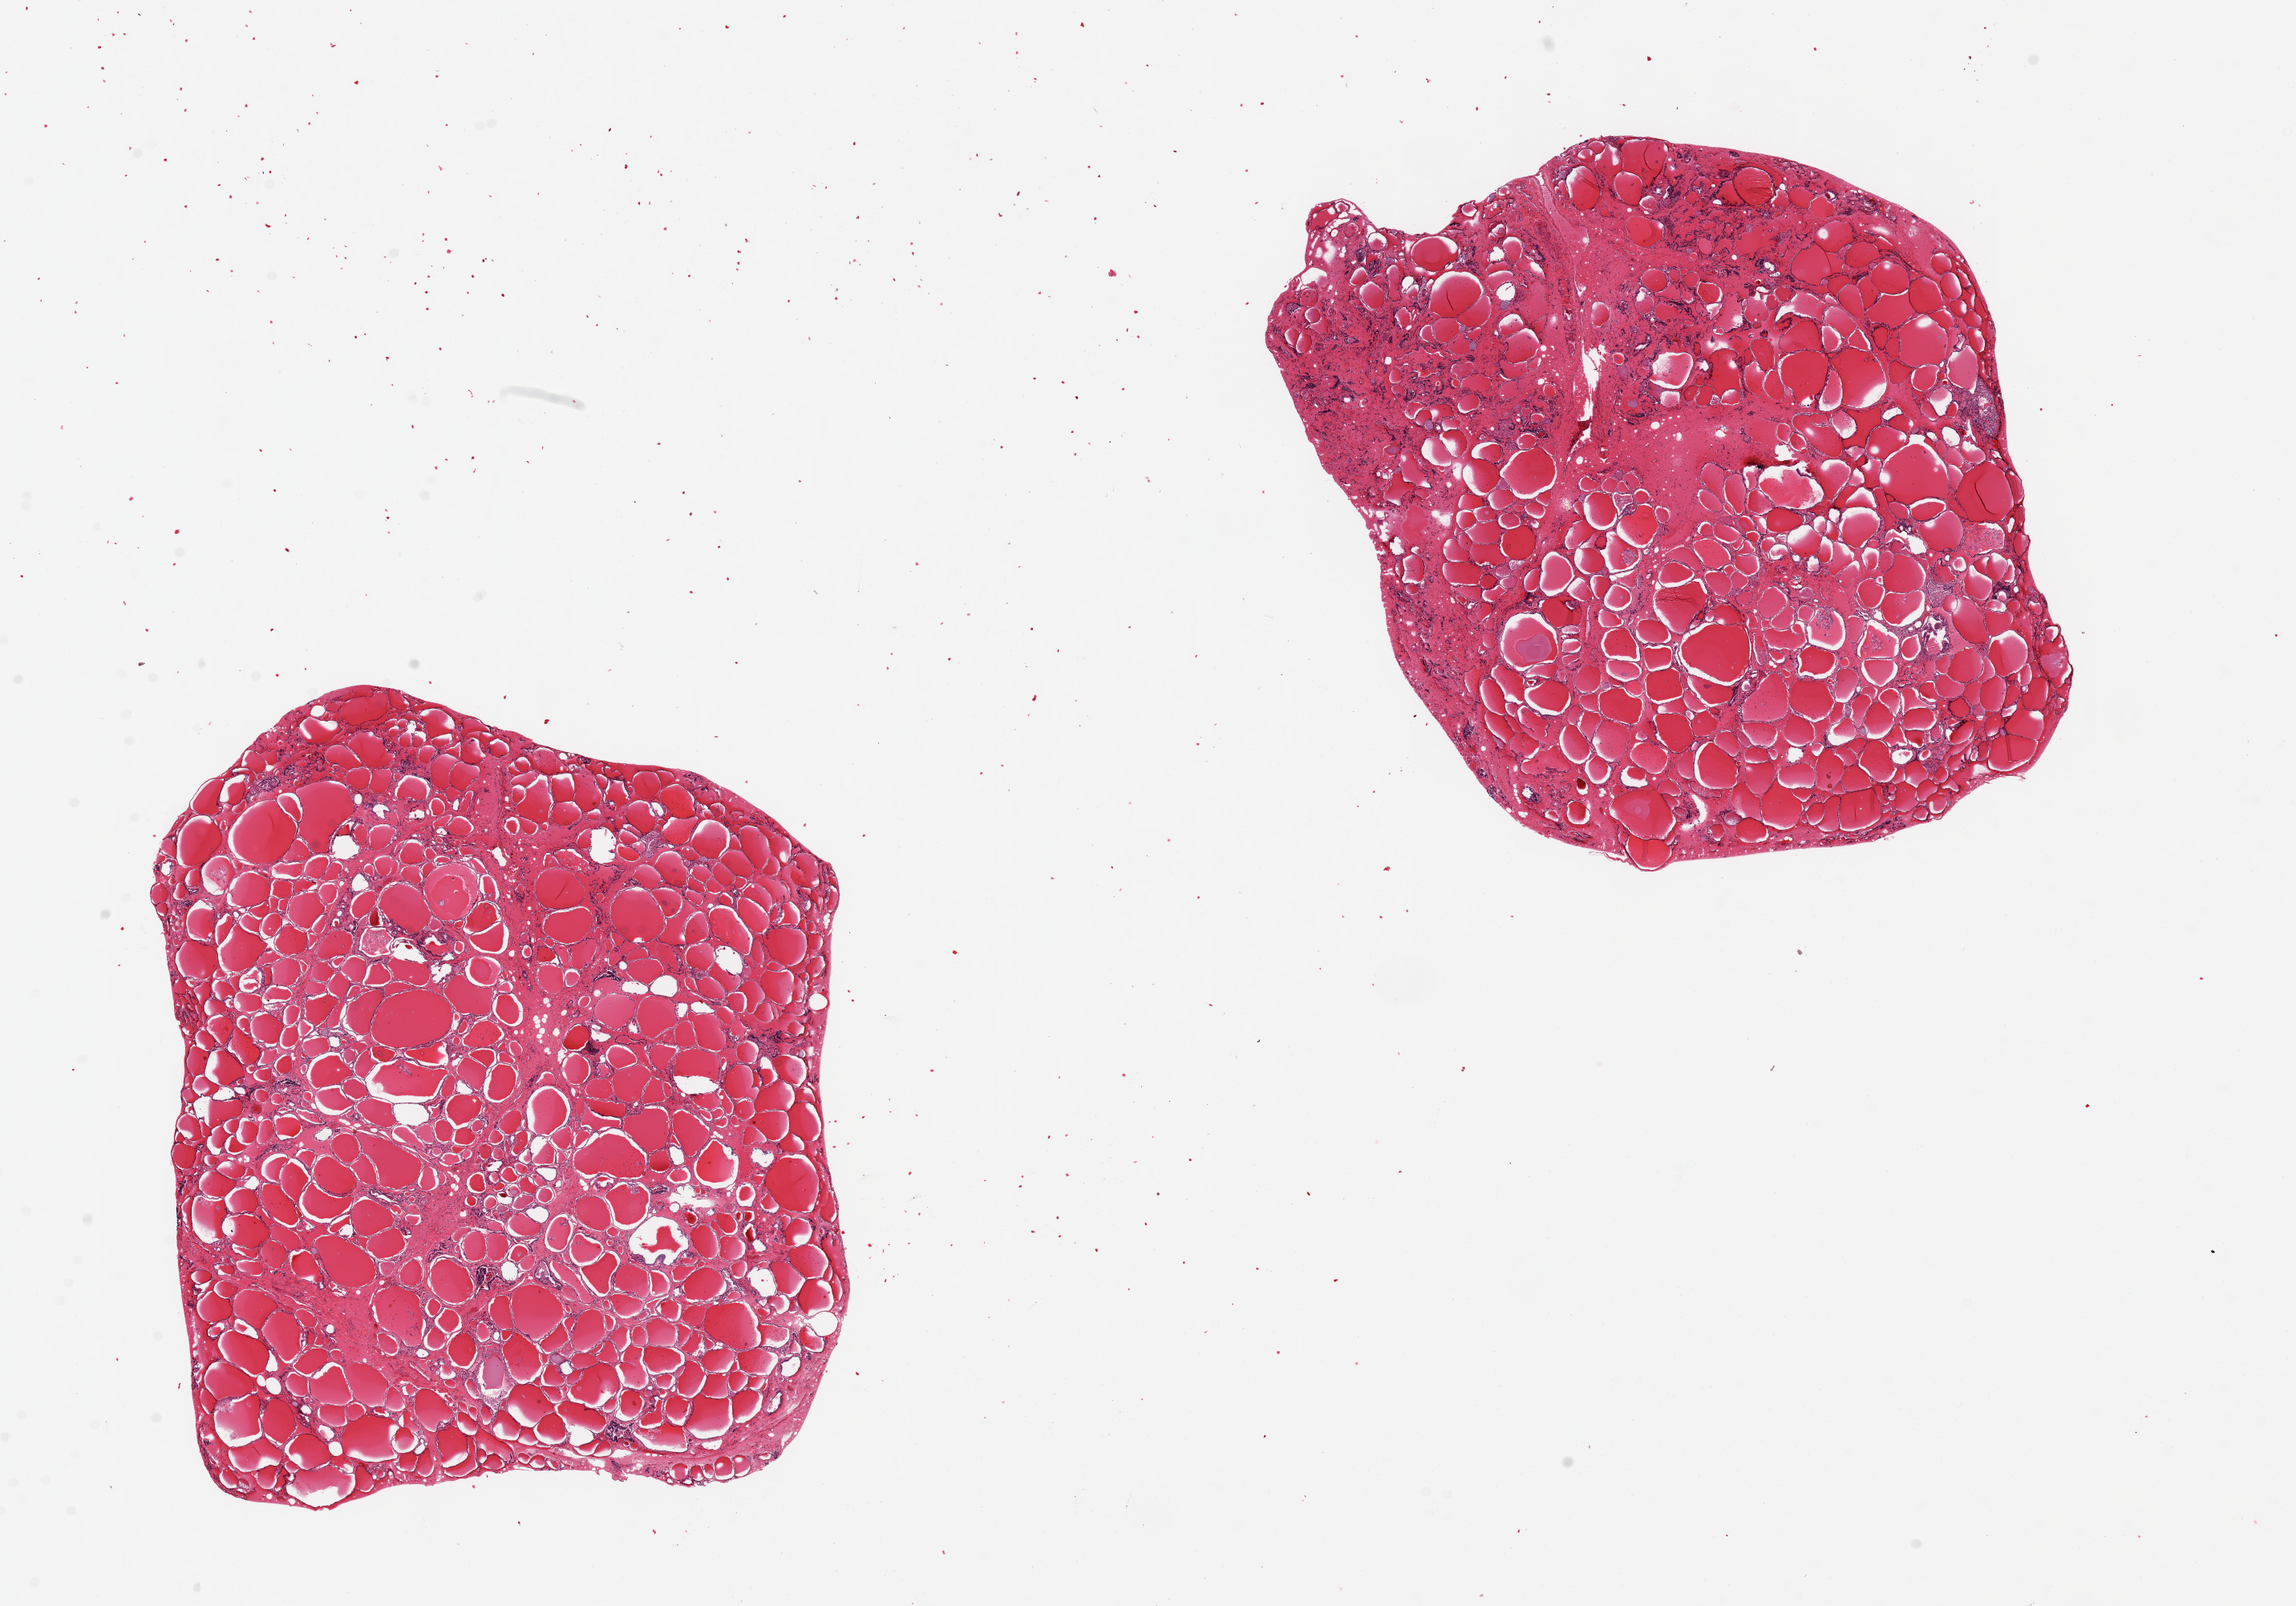
Whole-slide image, haematoxylin and eosin stain — low-resolution overview of the scanned area, about 22.6 x 15.8 mm (from a 20x scan); PAXgene-fixed paraffin-embedded (PFPE) section; sampled site (target tissue): thyroid; tissue donor sample. Female donor.
Pathologist's review note for this sample: 2 pieces, 8x7 & 7x7mm.